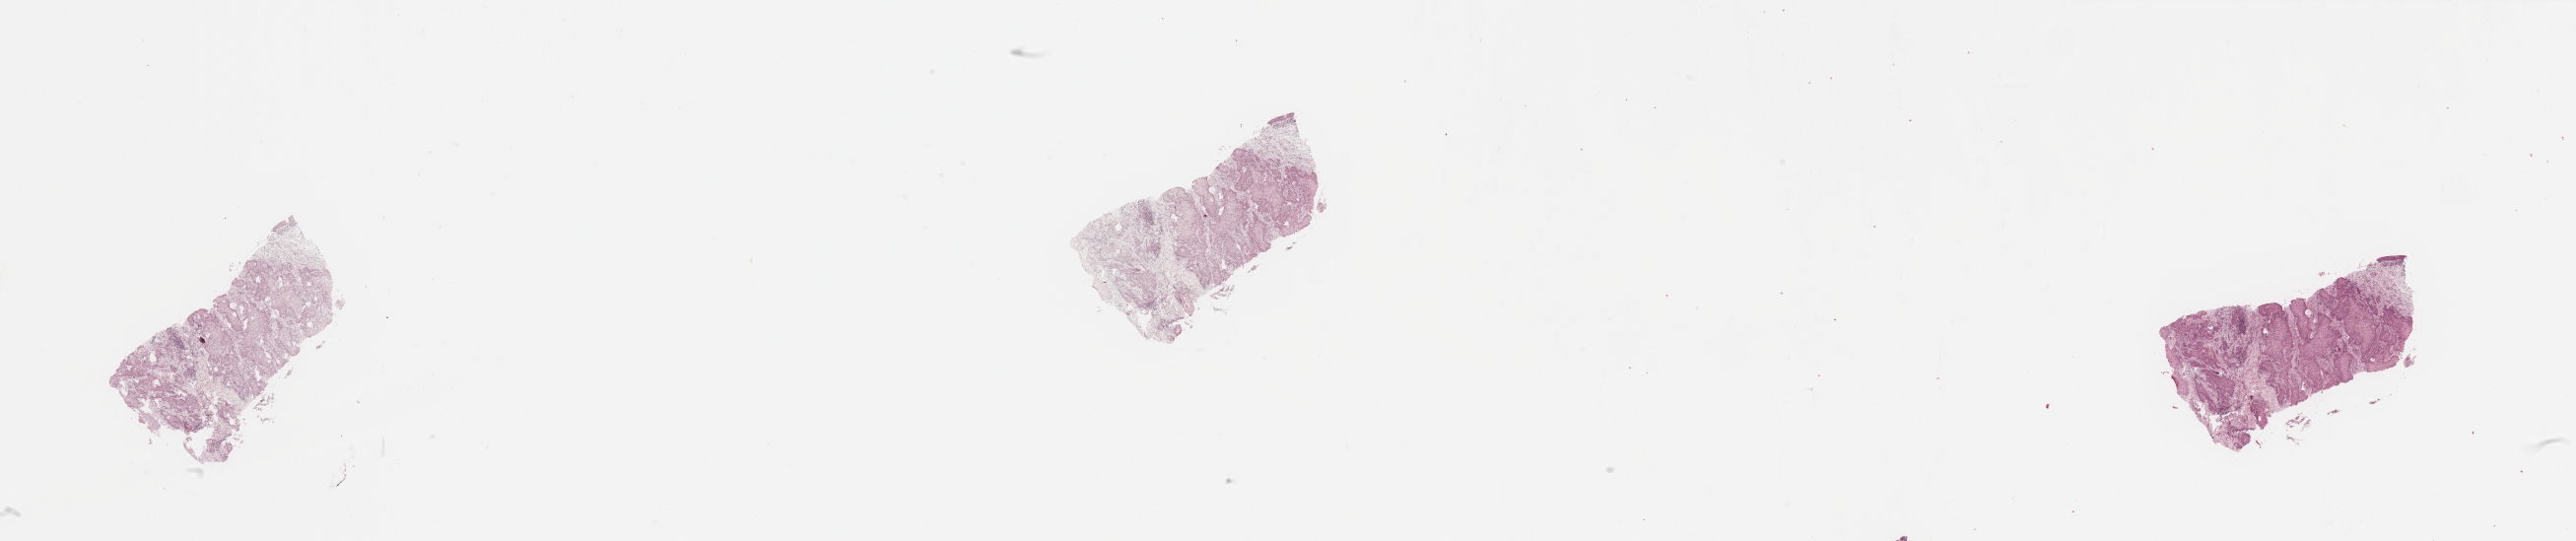
Digitized H&E tissue section (whole slide) — whole scanned area (about 41.3 x 8.7 mm) shown as a low-resolution overview, tumour tissue sample, sampled site: larynx. Patient: male, age 68 years. Histologic grade: G2 (moderately differentiated). Slide review estimates, as recorded: tumour nuclei 80%, necrosis 5%.
- histologic diagnosis: Squamous cell carcinoma, NOS (larynx, NOS)
- AJCC pathologic stage: IVA
- primary tumour site (as recorded): larynx